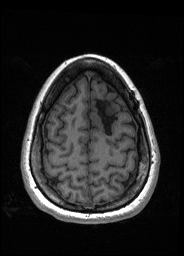
Pre-operative brain MRI before brain-tumour surgery, one axial slice. Position 47 of 176 along the scan axis. T1-weighted post-contrast. 1 mm slice thickness. 184 × 256 image matrix, field of view 180 × 250 mm. Case-level facts recorded for this patient, not image findings: histopathology: Oligodendroglioma; WHO grade: 2; IDH mutation: yes.
Outlined on this slice (expert manual segmentation):
- tumour: box from (x=91, y=104) to (x=116, y=125) px